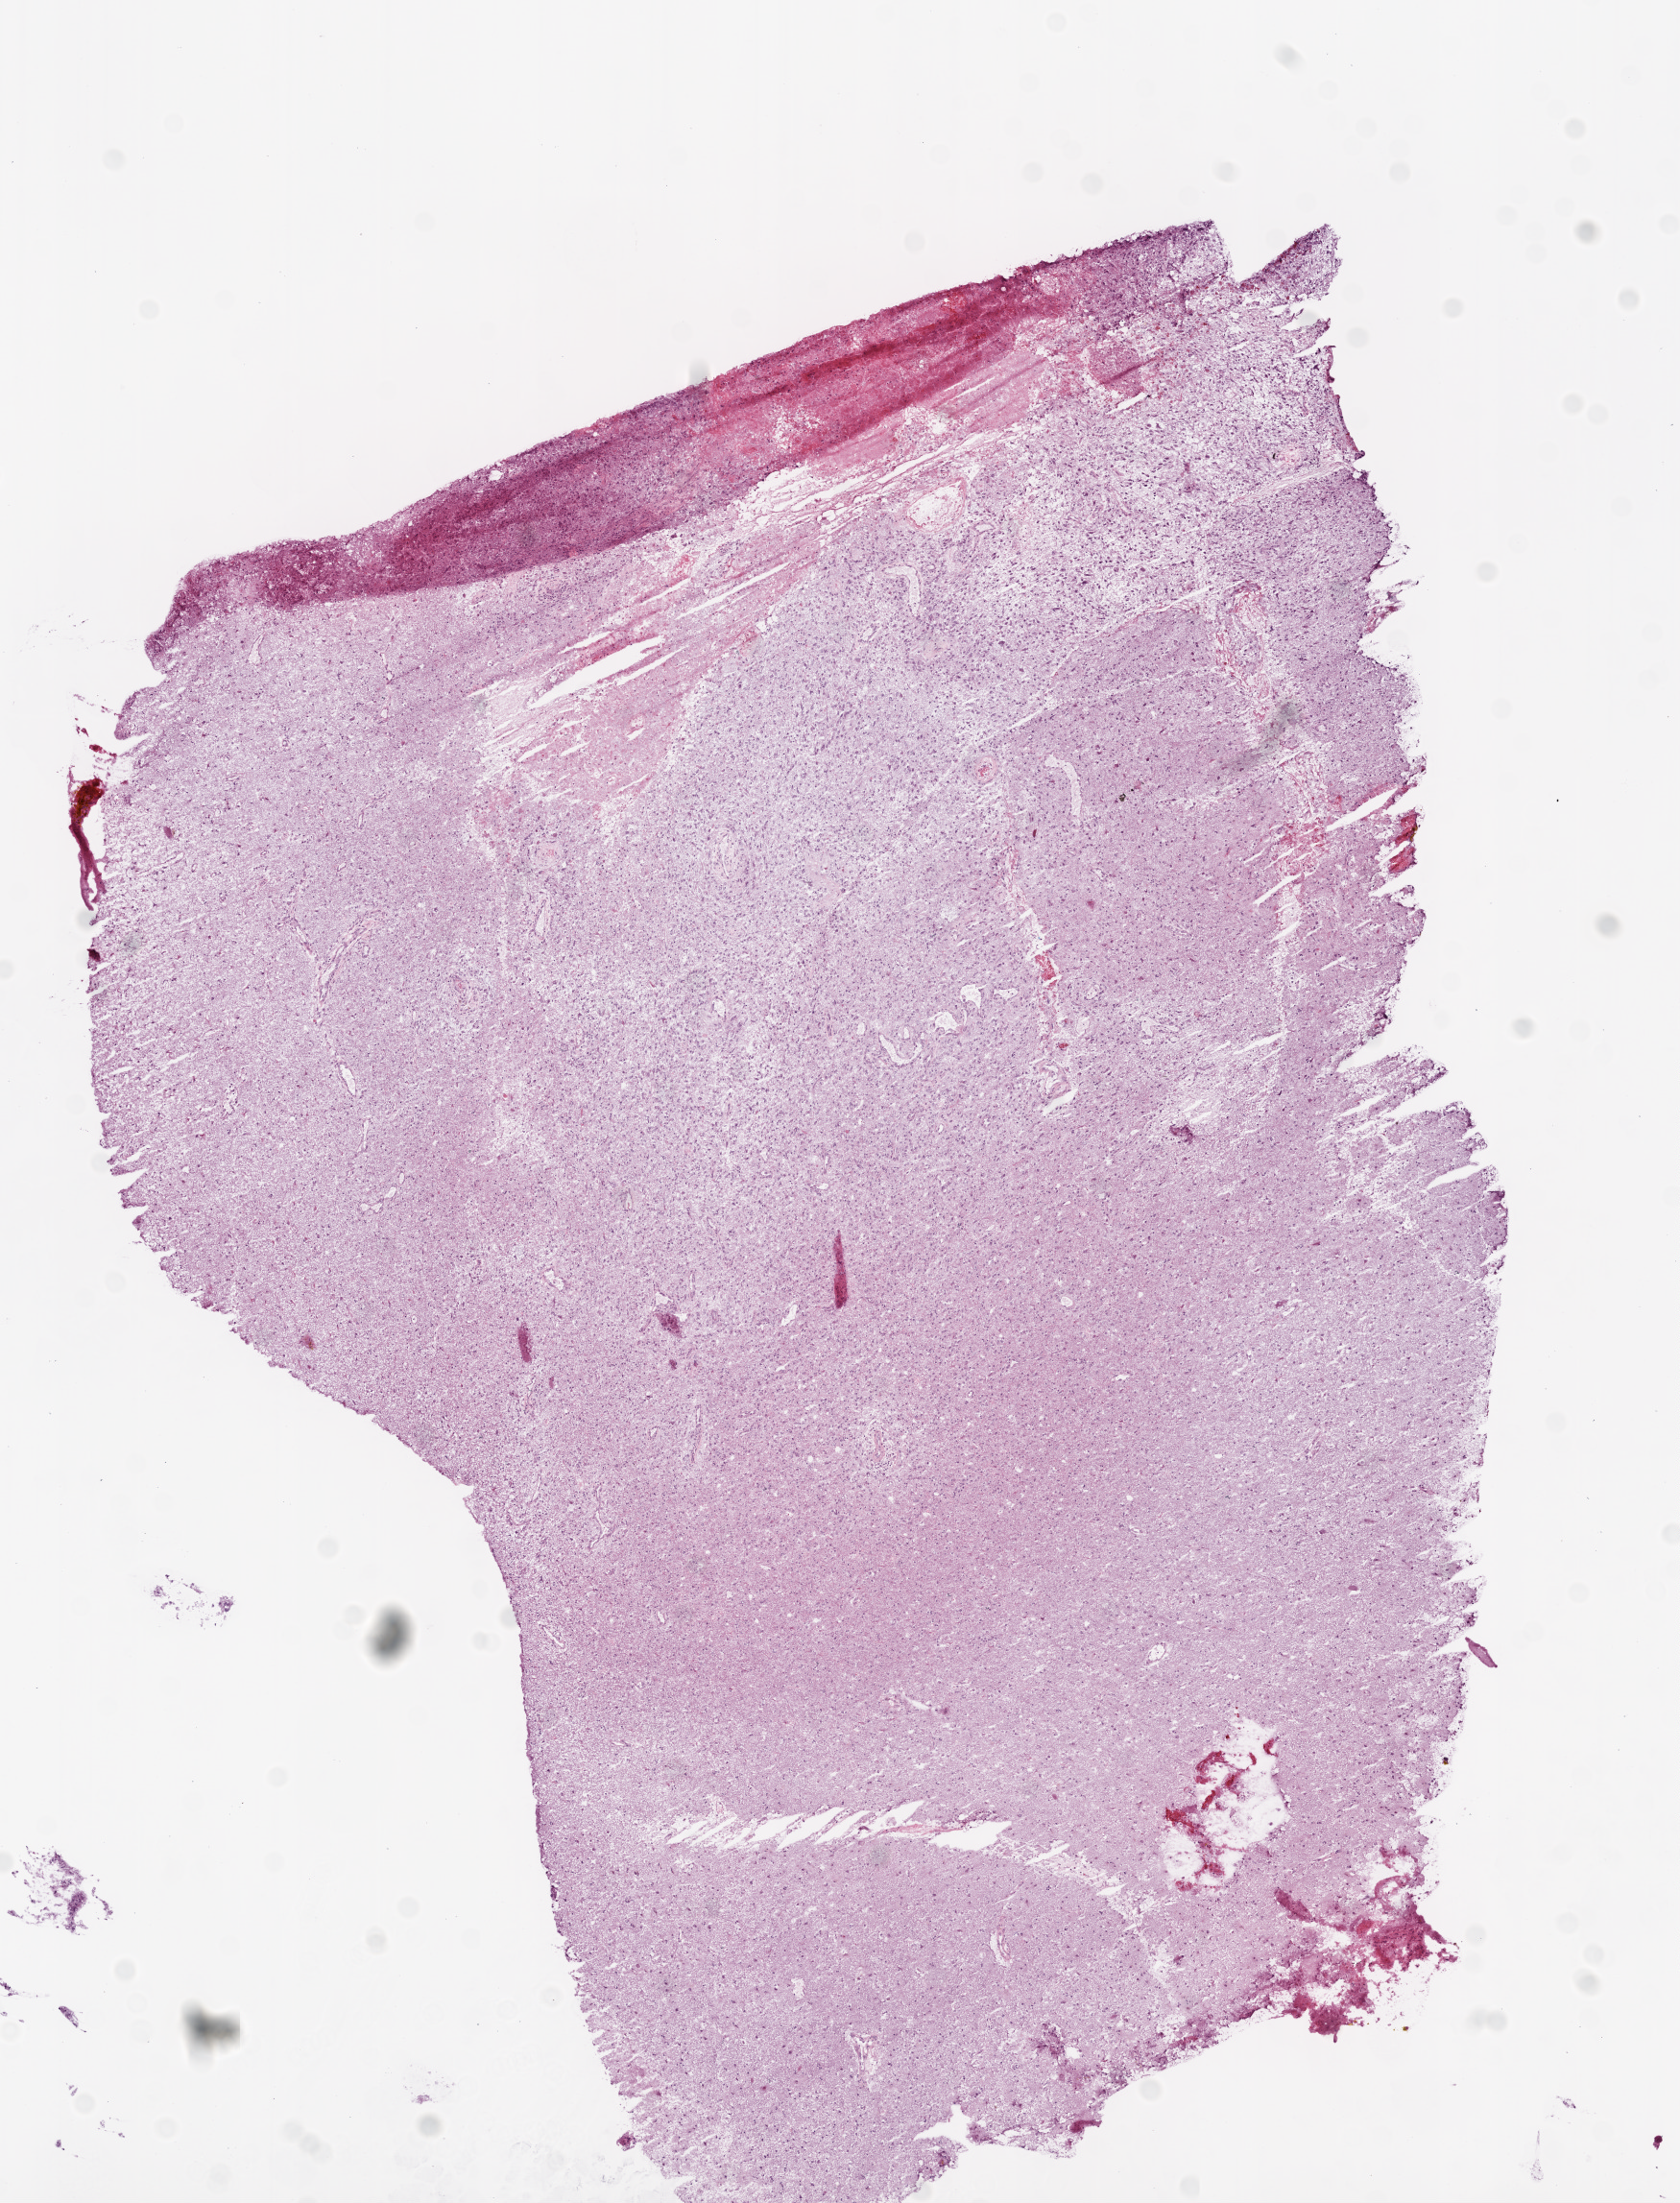
H&E whole-slide image — a low-resolution overview of the entire scanned area, about 7.0 x 9.2 mm, frozen section from the top of the tissue portion, sample: primary tumour, brain. Male patient; age at initial diagnosis 72 years. Composition of this section per pathologist review: tumour cells 50%, tumour nuclei 60%, normal cells 40%, stromal cells 0%, necrosis 10%.
Histologic diagnosis: Glioblastoma.